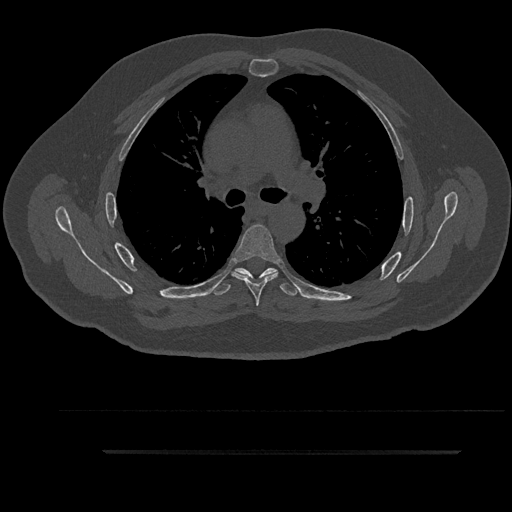
CT including the spine, one axial slice; bone window (W 1800 / L 400 HU); 0.5 mm slice thickness; 512 × 512 image matrix. Male patient, age 63 years. From the clinical record (not read from this slice): primary cancer: renal; vertebrae with lytic lesions (as recorded): T8.
Outlined on this slice (semi-automatic segmentation, software-assisted and operator-edited):
- T5 vertebra: bounding box [x1, y1, x2, y2] px = [232, 224, 281, 306]
- T6 vertebra: [212, 268, 299, 296]